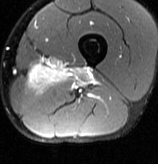
MRI of an extremity soft-tissue mass, one axial slice. Position 21 of 70 along the scan axis. T2-weighted fat-saturated. MR volume resampled by the dataset authors to the PET/CT grid (not the native acquisition matrix). 3.27 mm slice thickness. 158 × 164 image matrix, field of view 154 × 160 mm. Male patient. Case-level facts recorded for this patient, not image findings: histological type: extraskeletal osteosarcoma; grade: high; site of the primary tumour: left adductur.
Structures marked on this image (expert contour drawn on MRI and transferred to this co-registered scan by the dataset authors):
- gross tumour volume (mass): box from (x=26, y=64) to (x=96, y=93) px